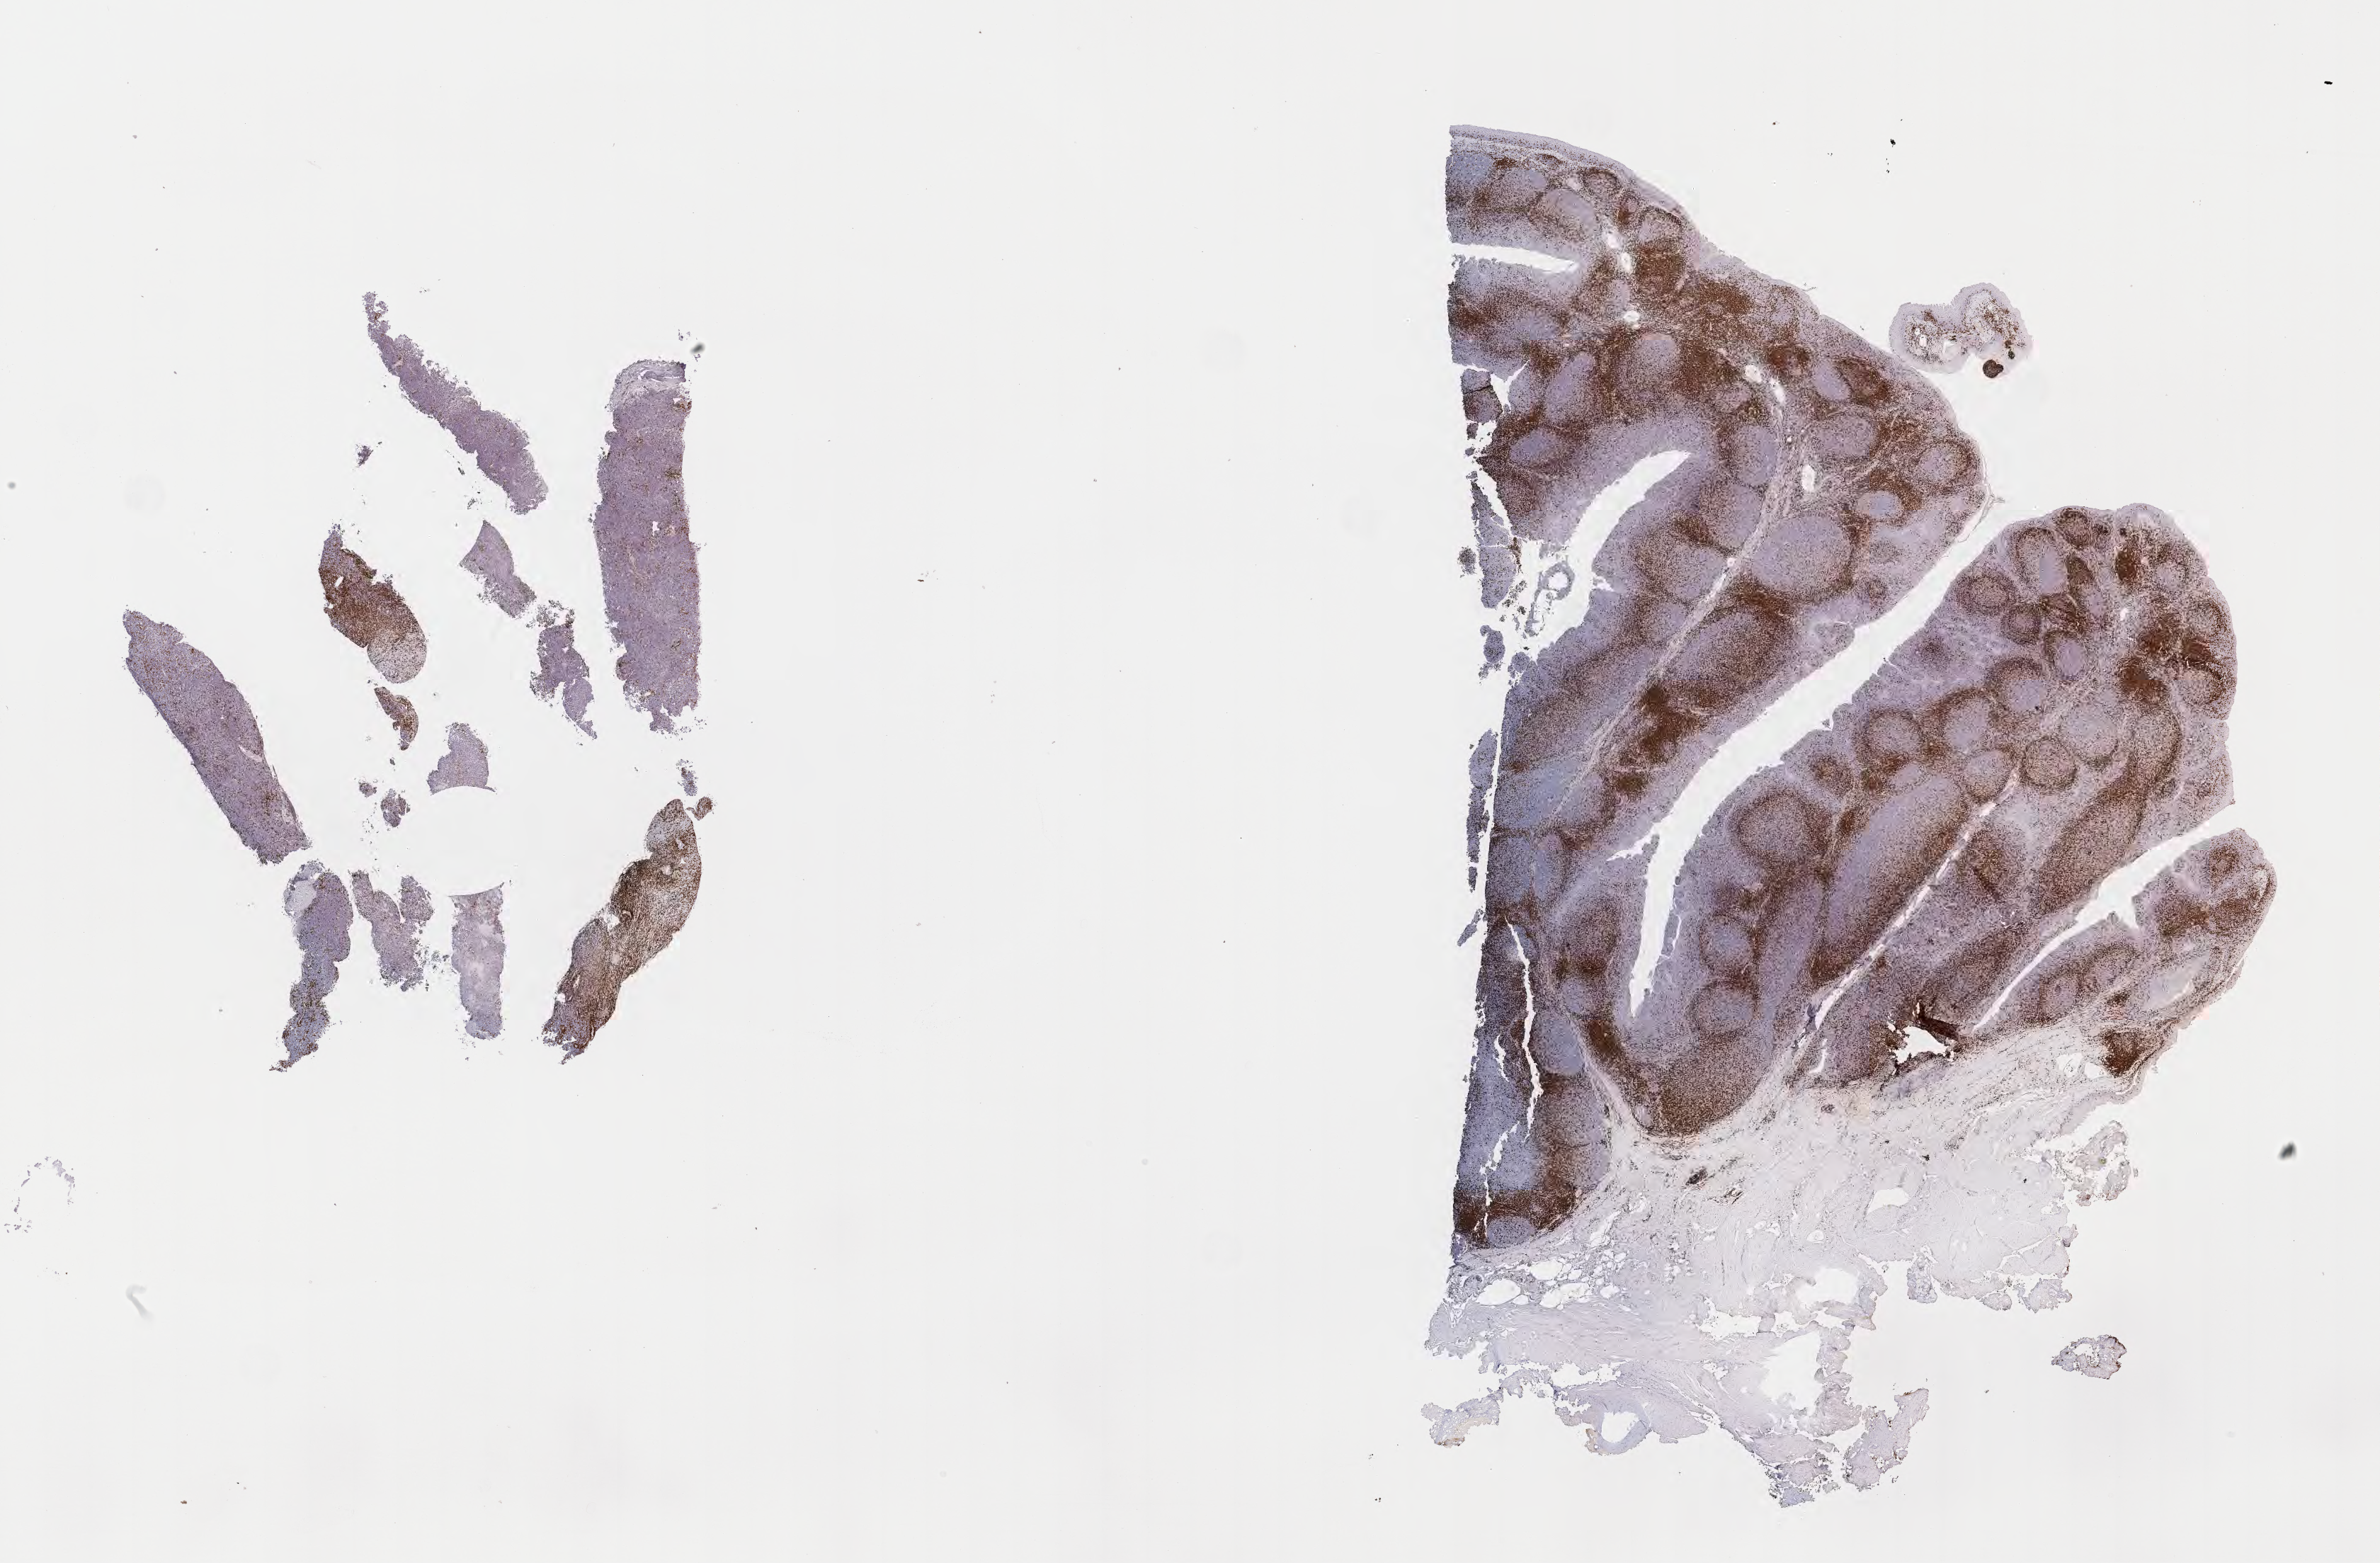
Immunohistochemistry (IHC) whole-slide image stained for CD3 — a low-resolution overview of the entire scanned area, about 27.2 x 17.8 mm, specimen: tumor tissue, site: abdomen proper. Patient: male, age at initial diagnosis 7 years.
- diagnosis: Burkitt lymphoma, NOS